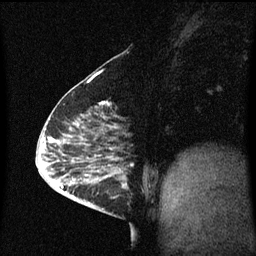
Breast MRI (dynamic contrast-enhanced), one sagittal slice. Slice 23 of 60 in the series (ordered by position). Dynamic contrast-enhanced series, image 2 of 3 at this slice position (ordered by acquisition). 1.5 T. TE 4.2 ms, TR 8.4 ms. 2 mm slice thickness. 256 × 256 image matrix. Patient: female, 63 years.
Outlined on this slice (semi-automatic segmentation, software-assisted and operator-edited):
- analysis volume of interest (the breast-tissue region the enhancement analysis was run in; not a lesion): bounding box [x1, y1, x2, y2] px = [98, 168, 133, 217]
- tumour enhancement mask (voxels above the 70 % enhancement threshold inside the analysis volume of interest): [98, 170, 127, 199]